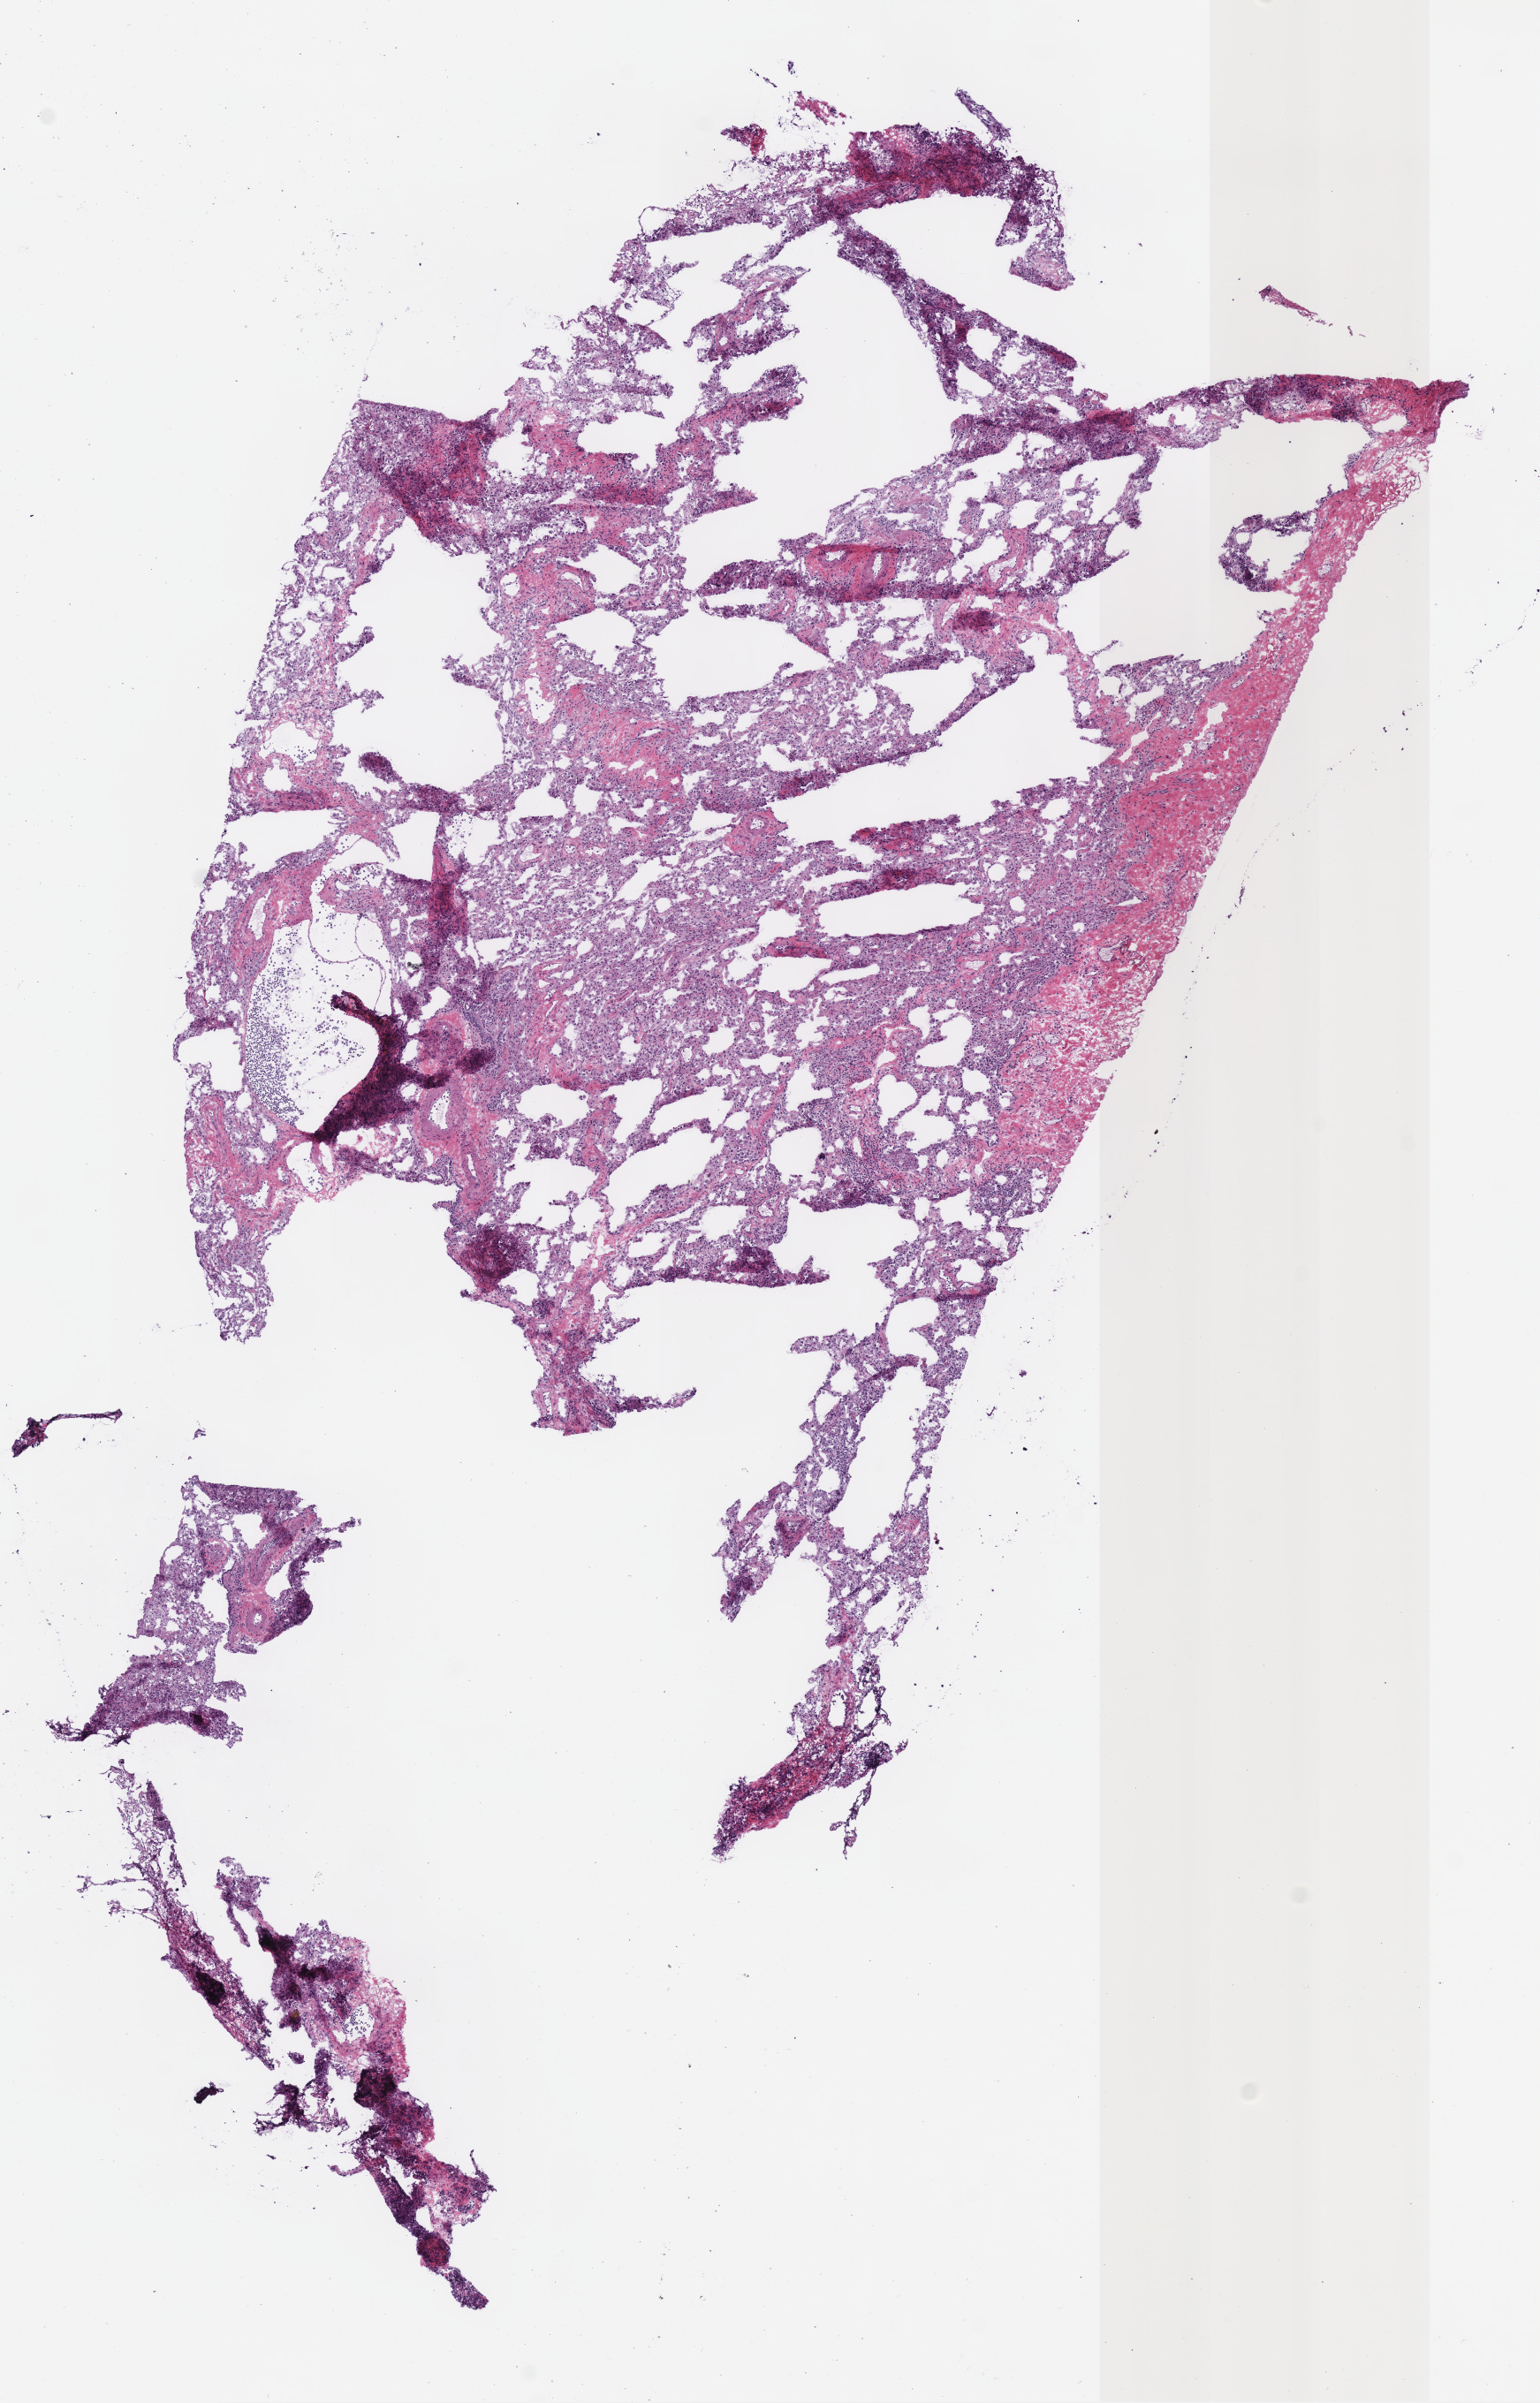
Whole-slide histology image, H&E-stained, low-resolution overview of the scanned area, about 6.9 x 10.7 mm (slide scanned at 40x), frozen section, lung, solid tissue normal (non-tumour tissue) sample. Male patient; age at initial diagnosis 60 years. Inflammatory infiltration, as recorded: lymphocyte infiltration 2%, monocyte infiltration 10%.
• this section: solid tissue normal sample (biorepository sample class)
• patient diagnosis: Basaloid squamous cell carcinoma (upper lobe, lung)